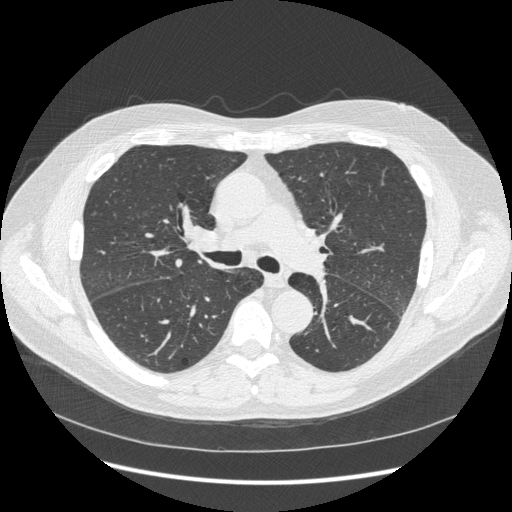
Chest CT (low-dose screening protocol), one axial image. Second annual screen. Lung window (W 1500 / L -600 HU). 512 × 512 image matrix, field of view 389 × 389 mm. Male participant, aged 59 years at enrolment. Current smoker at enrolment.
Lesion marked by an expert reader, bounding box <176,215,235,258> (left, top, right, bottom; pixels). Reader record for this screening exam (exam-level; its link to the box is not recorded): non-calcified nodule or mass ≥4 mm, lingula, 5 × 5 mm, smooth margins, soft tissue attenuation, pre-existing on the prior screen: yes; interval growth: no. Note: the box lies in the patient's right hemithorax on this image, whereas the reader's record names the left lung; they may be different findings. Official screen result: positive, change unspecified: nodule(s) >= 4 mm or enlarging nodule(s), mass(es), or other non-specific abnormalities suspicious for lung cancer. Lung cancer was diagnosed 540 days after this screen: squamous cell carcinoma, keratinizing, NOS, right hilum, stage IIIB (AJCC 6th edition).